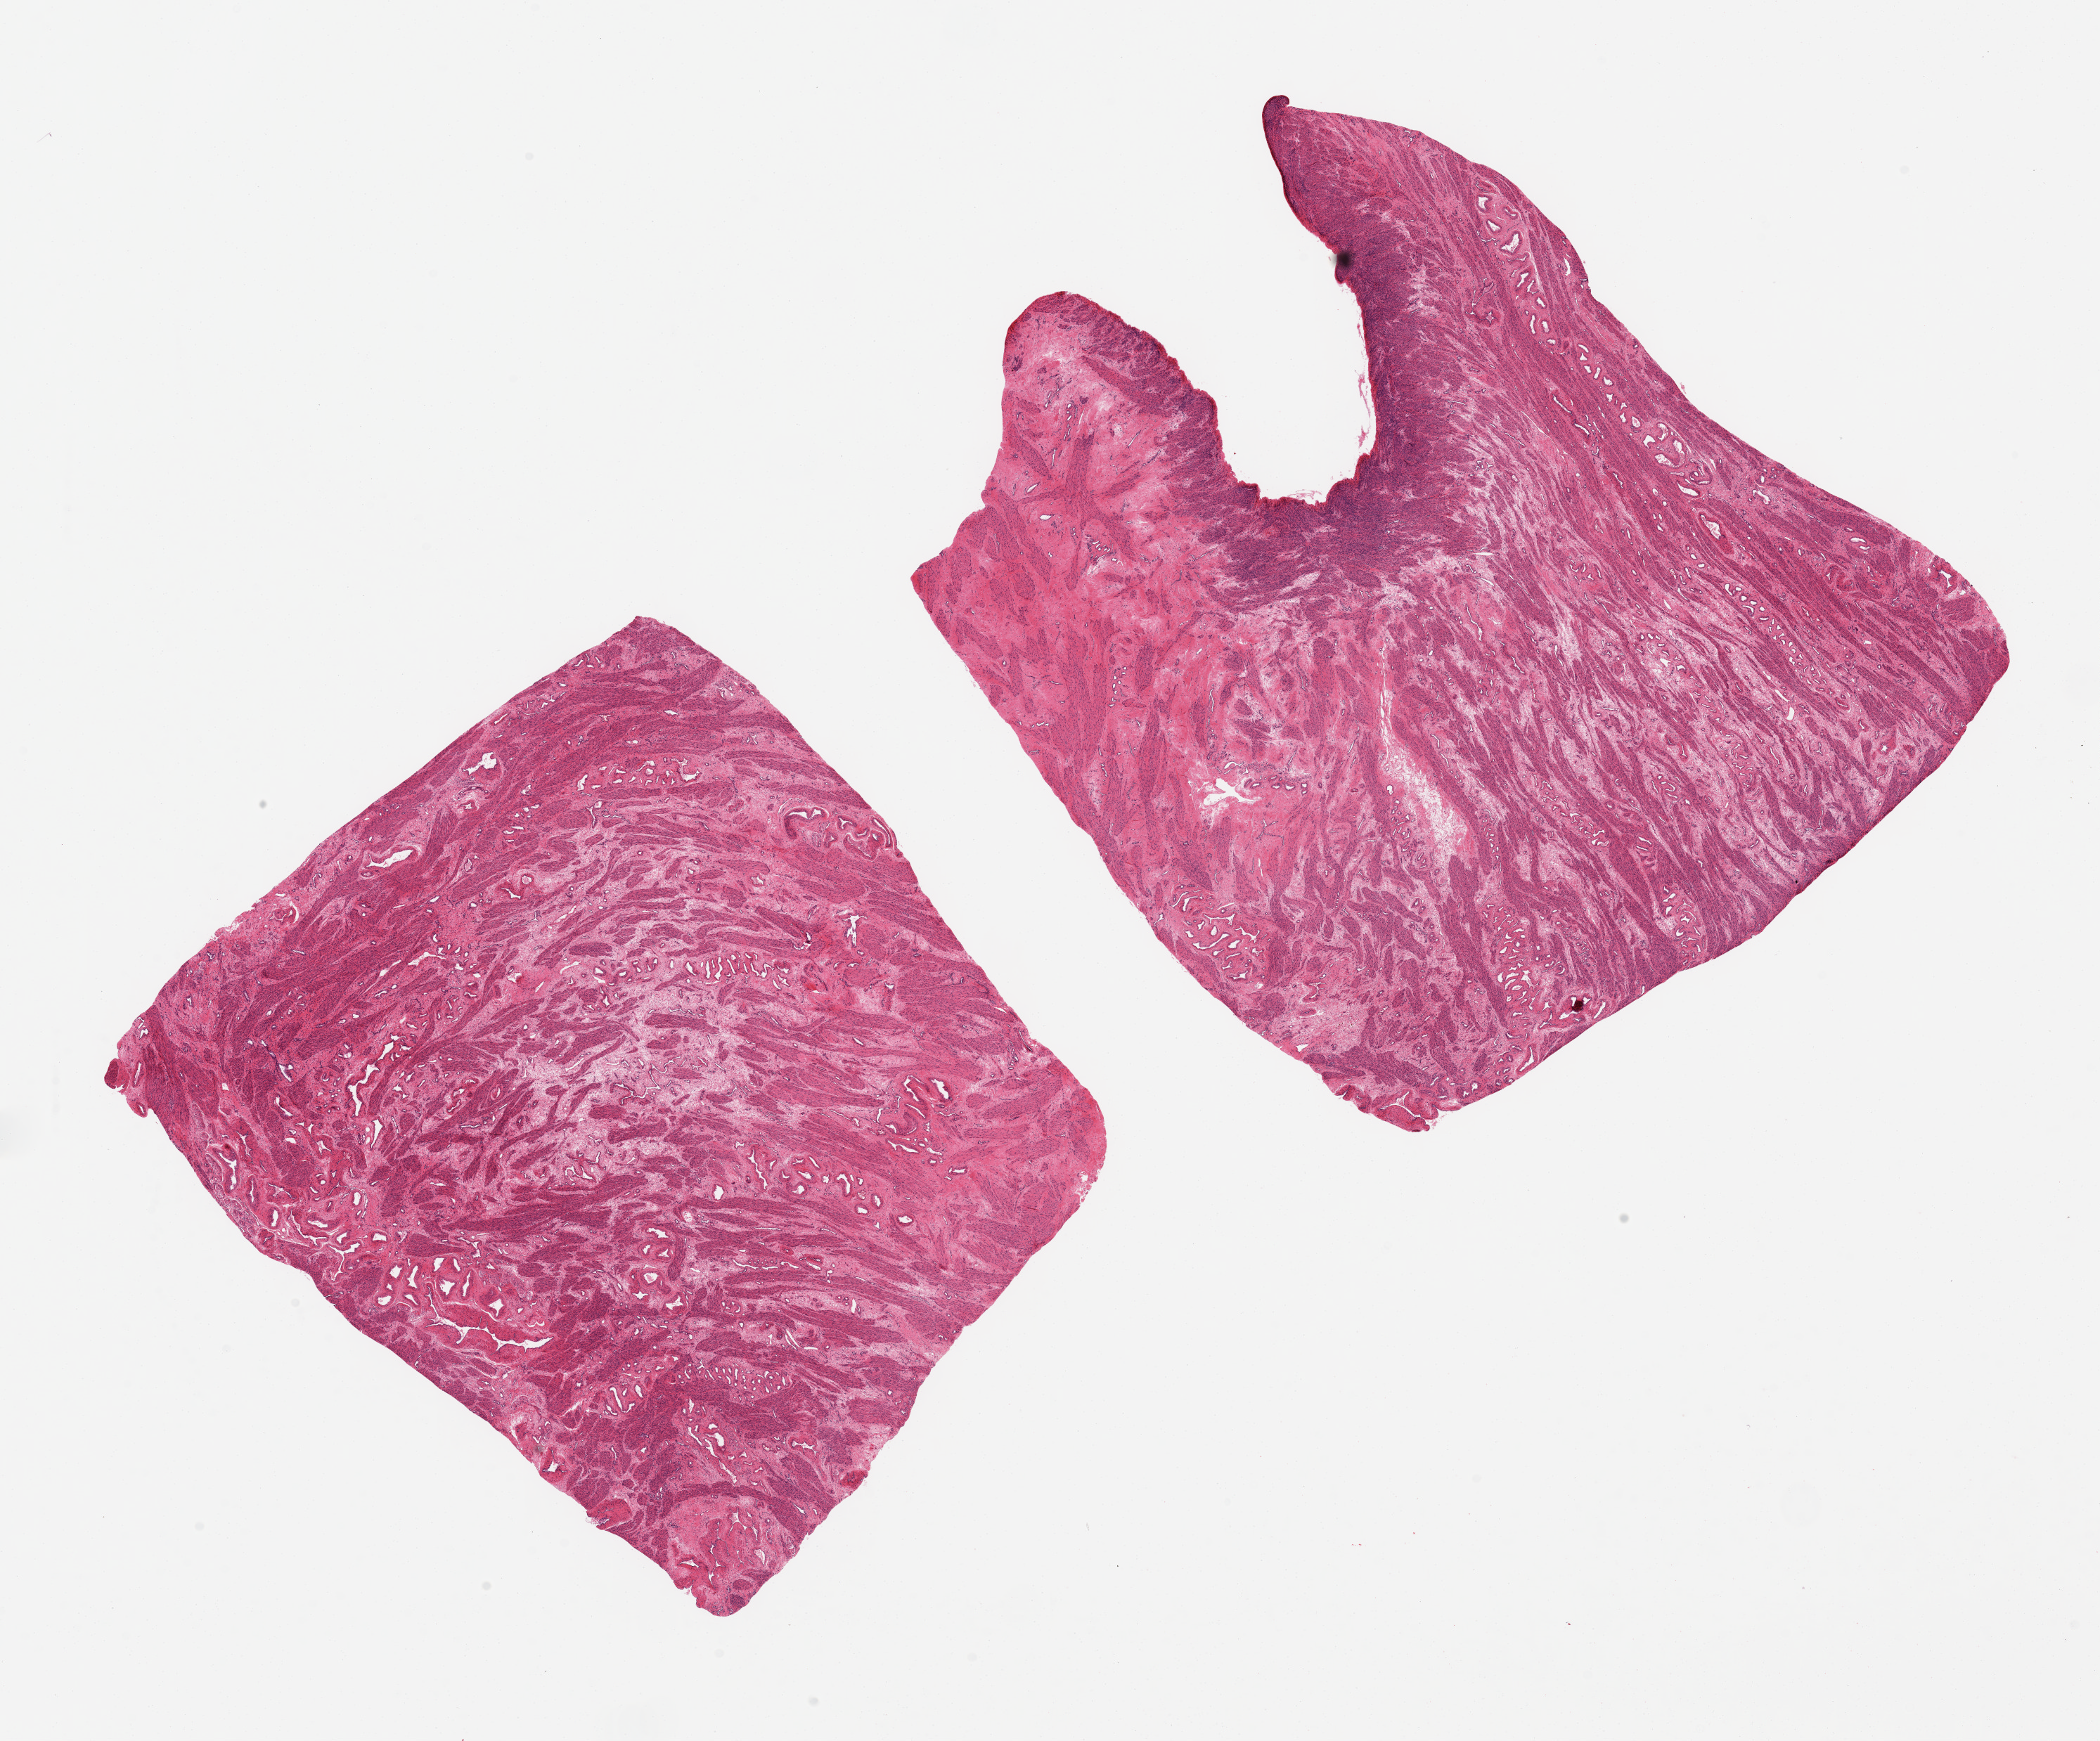
Whole-slide image, H&E stain, whole scanned area (about 23.6 x 19.6 mm) shown as a low-resolution overview, PAXgene-fixed paraffin-embedded (PFPE) section, section of uterus (target tissue), donor tissue sample. Female donor.
Pathologist's review note for this sample: 2 pieces, 10x9 & 9x8 mm; no glands present.